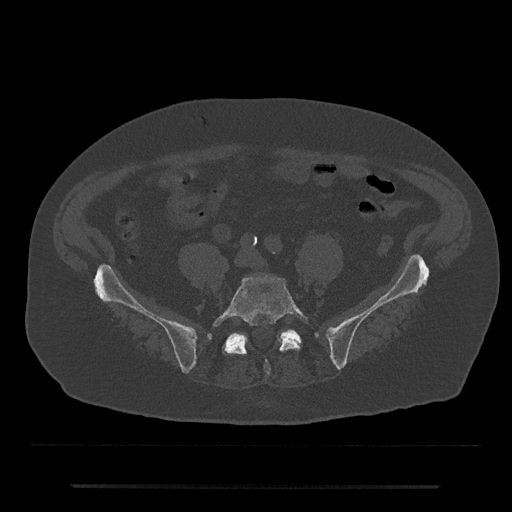
CT including the spine, one axial slice. 120 kVp. Bone window (W 1800 / L 400 HU). 512 × 512 image matrix, field of view 434 × 434 mm. Male patient, age 80 years. From the clinical record (not read from this slice): primary cancer: prostate; vertebrae with lytic lesions (as recorded): L1, T11.
Outlined on this slice (semi-automatically segmented with operator editing):
- L5 vertebra: bounding box [x1, y1, x2, y2] px = [212, 276, 308, 374]